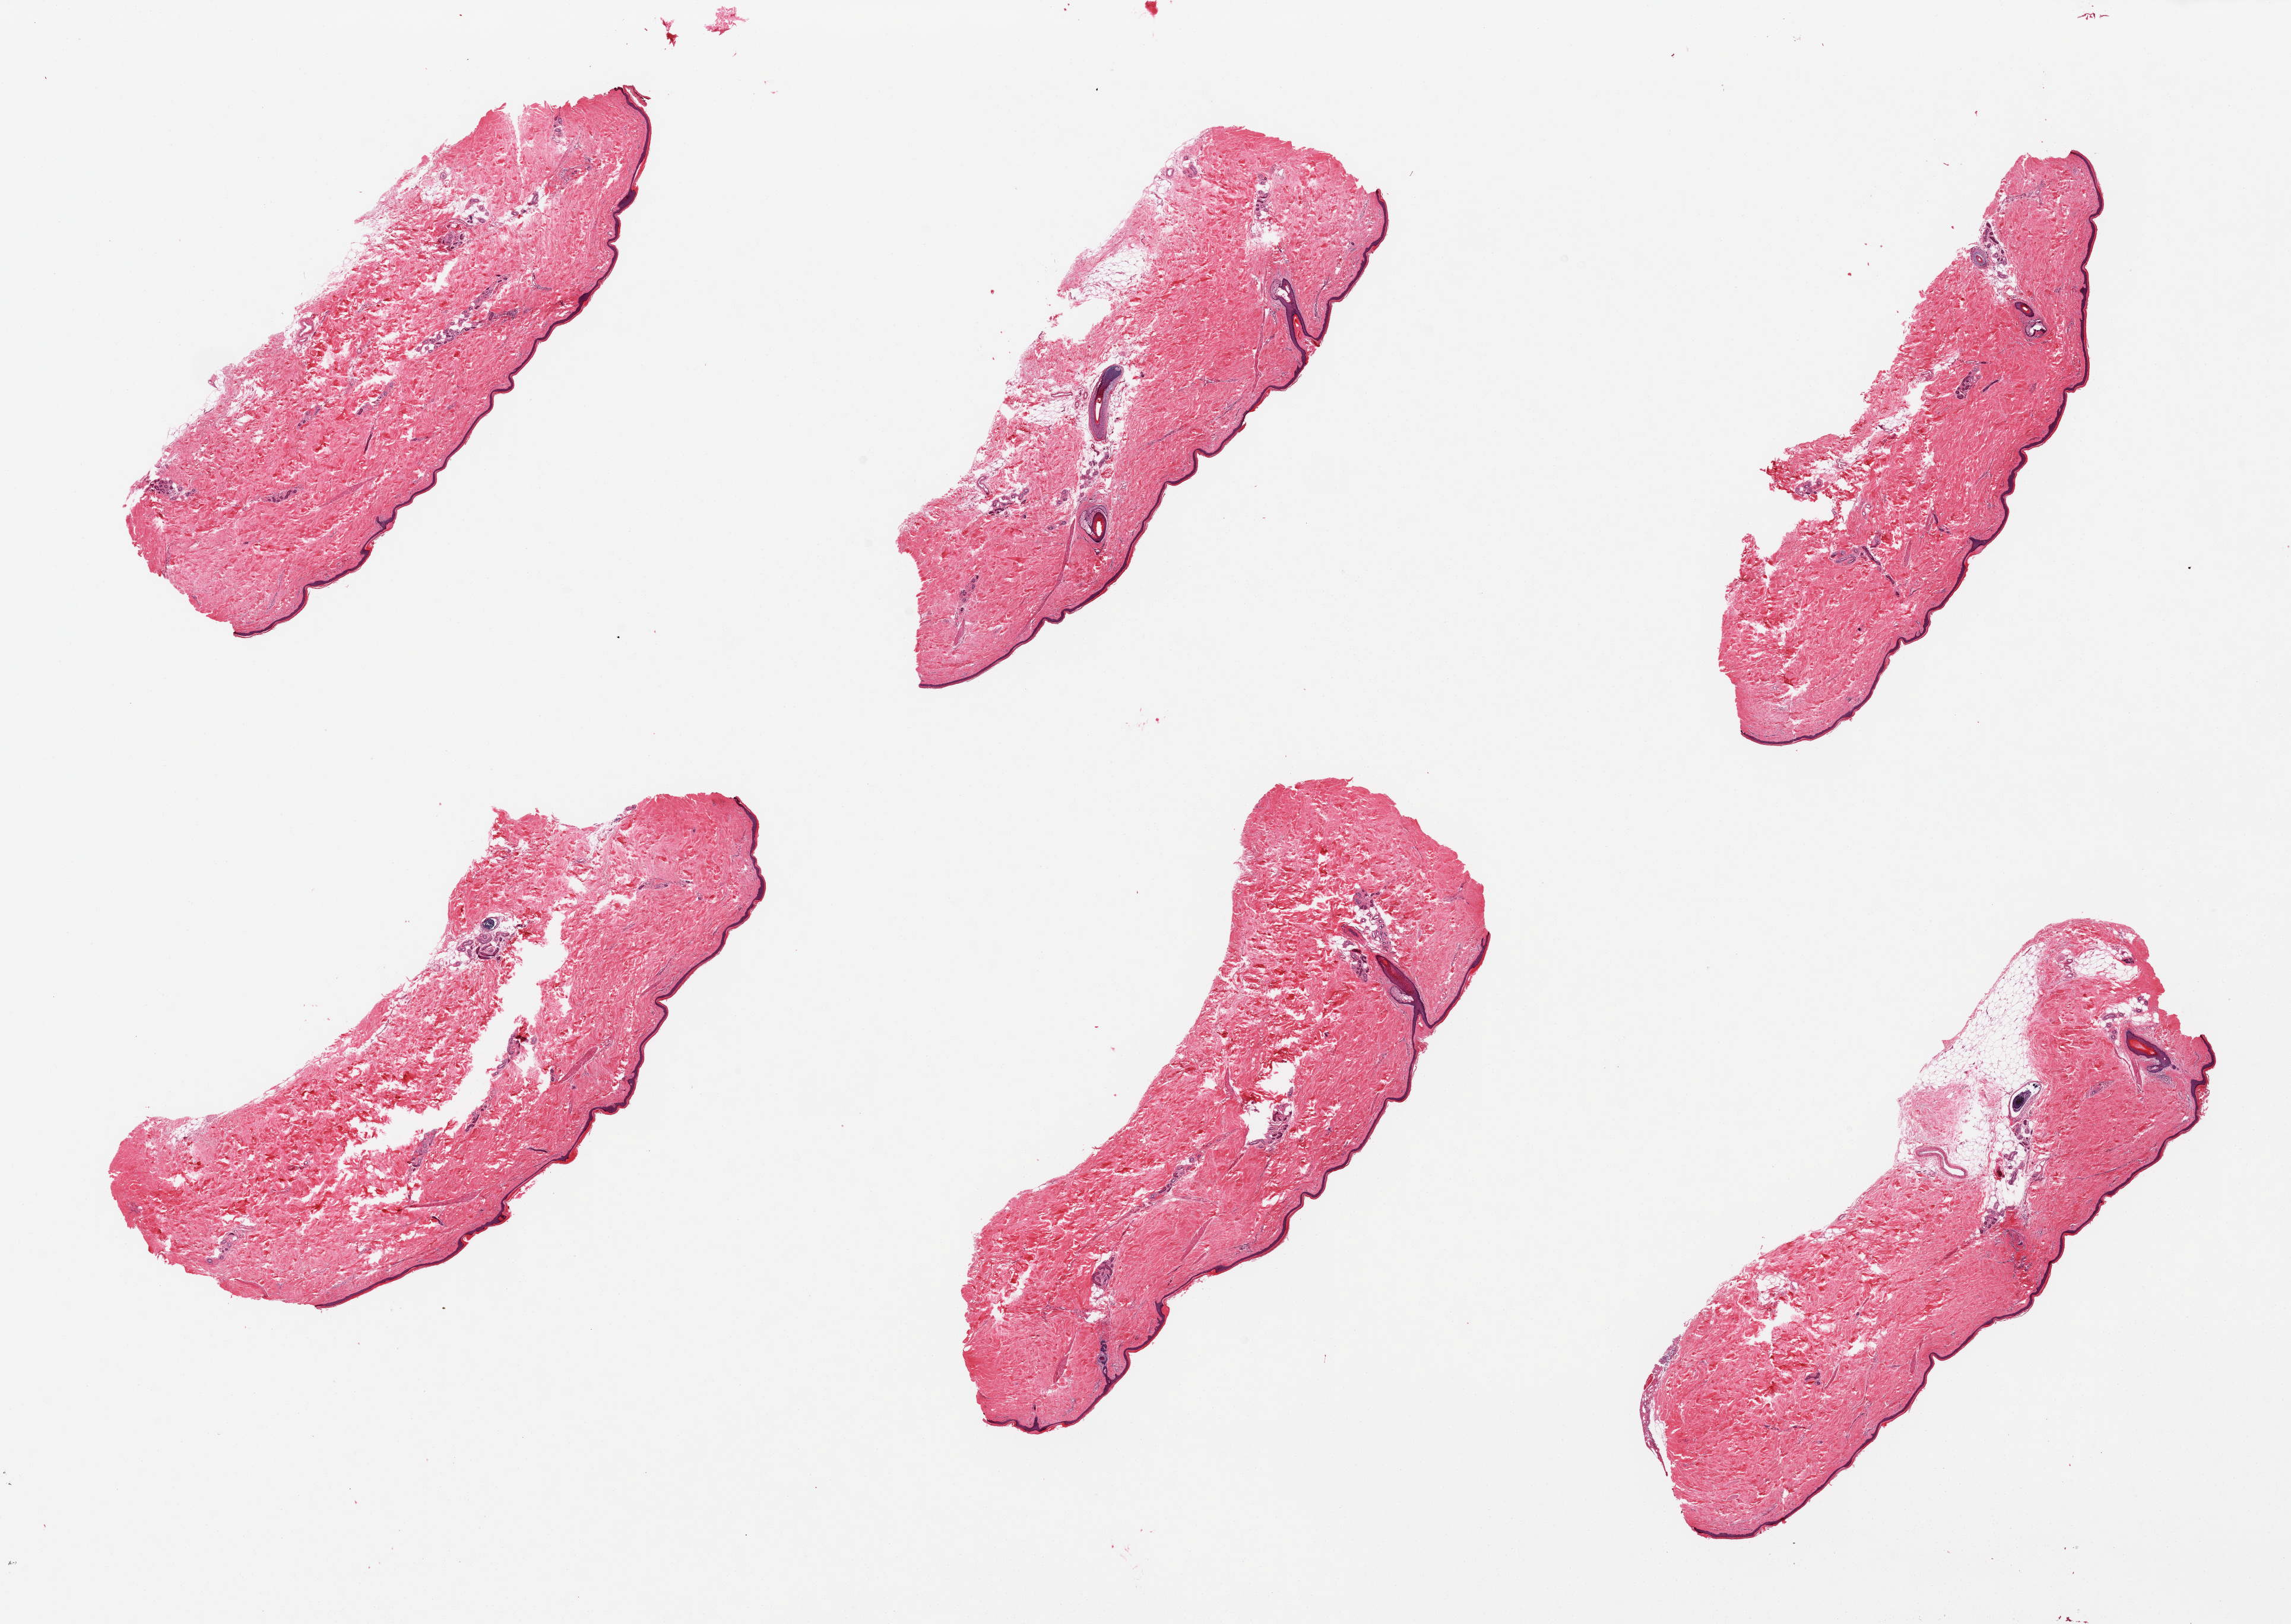
Whole-slide image, H&E stain, a low-resolution overview of the entire scanned area, about 30.5 x 21.6 mm. PAXgene-fixed, paraffin-embedded tissue. Section of skin of lower leg (target tissue). Donor tissue sample.
• review note (as recorded): 6 pieces, predominantly well trimmed, one piece includes attached fat ~10%, squamous epithelium is ~30 microns thick